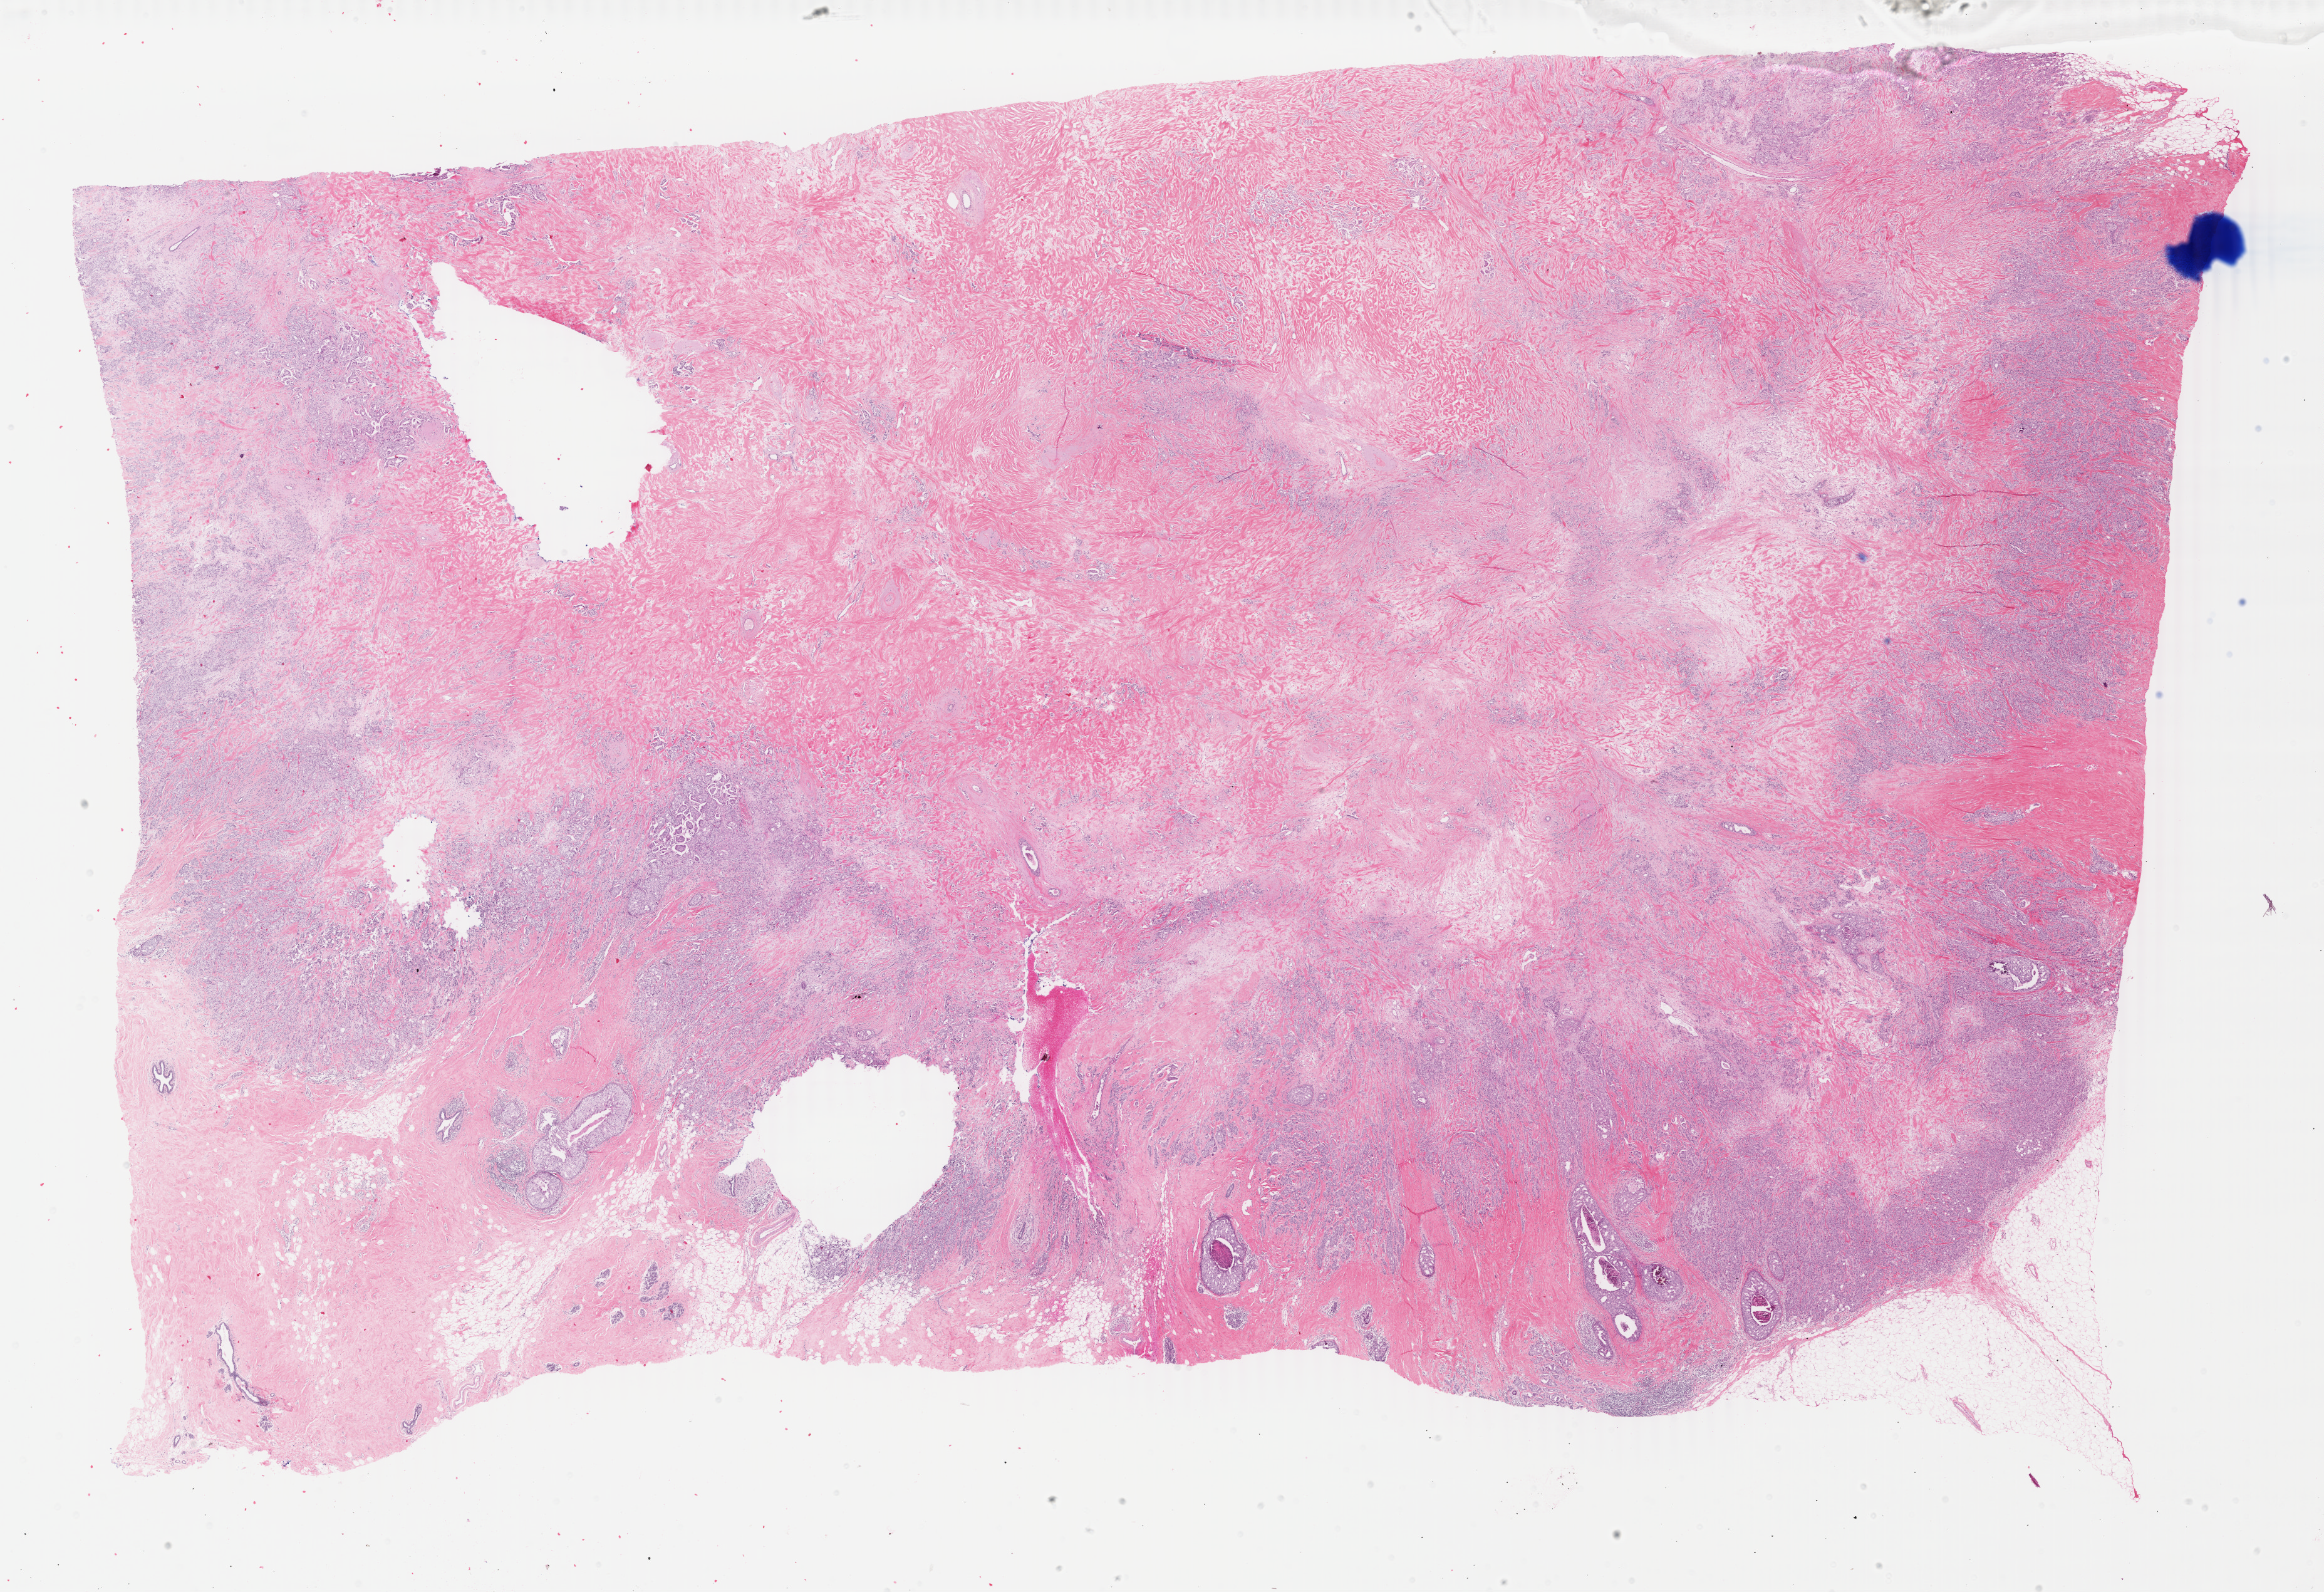
Whole-slide histology image, H&E-stained — whole scanned area (about 29.5 x 20.2 mm, from a 40x scan) shown as a low-resolution overview. Formalin-fixed paraffin-embedded (FFPE) diagnostic section. Breast, primary tumour sample. Patient: female, age at initial diagnosis 58 years.
Diagnosis: Infiltrating duct carcinoma, NOS.